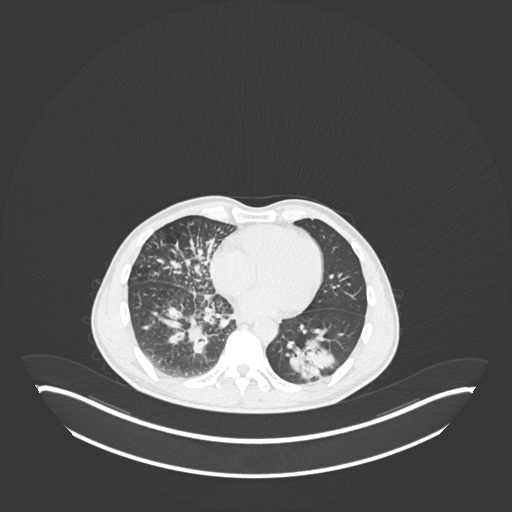
Chest CT, one axial slice. Slice 87 of 237 in the series (ordered by position). 120 kVp. Lung window (W 1500 / L -600 HU). 1 mm slice thickness. 512 × 512 image matrix. Male patient, age 49 years. From the clinical record (not read from this slice): clinical TNM (as recorded): T2b N1 M0.
Annotated regions visible in this slice (rectangle marked by the reading radiologist):
- lung tumour (recorded histology: adenocarcinoma): bounding box <286,336,338,385> (left, top, right, bottom; pixels)